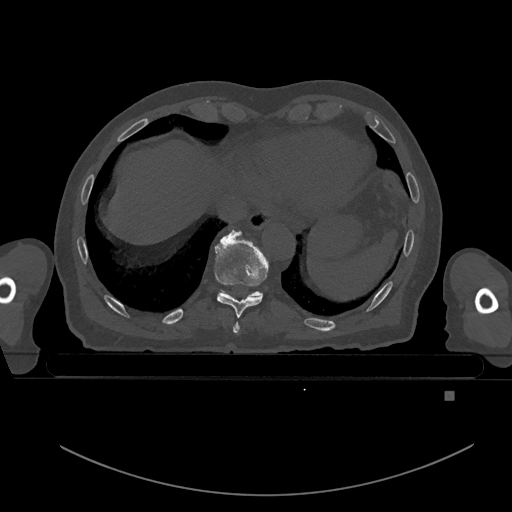
CT including the spine, one axial slice; slice 135 of 969 in the series (ordered by position); bone window (W 1800 / L 400 HU); 0.5 mm slice thickness; 512 × 512 image matrix. Male patient, age 82 years. From the clinical record (not read from this slice): primary cancer: prostate.
Annotated regions visible in this slice (semi-automatically segmented with operator editing):
- T10 vertebra: bounding box [x1, y1, x2, y2] px = [253, 291, 261, 296]
- T8 vertebra: [233, 322, 240, 333]
- T9 vertebra: [214, 230, 269, 318]